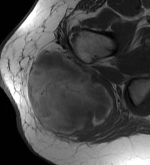
MRI of an extremity soft-tissue mass, one axial slice. MR volume resampled by the dataset authors to the PET/CT grid (not the native acquisition matrix). 3.27 mm slice thickness. 150 × 165 image matrix, field of view 146 × 161 mm. Female patient. From the clinical record (not read from this slice): histological type: epithelioid sarcoma with vascular differentiation; site of the primary tumour: right buttock.
Outlined on this slice (expert contour drawn on MRI and transferred to this co-registered scan by the dataset authors):
- gross tumour volume (mass): bounding box <25,47,115,139> (left, top, right, bottom; pixels)